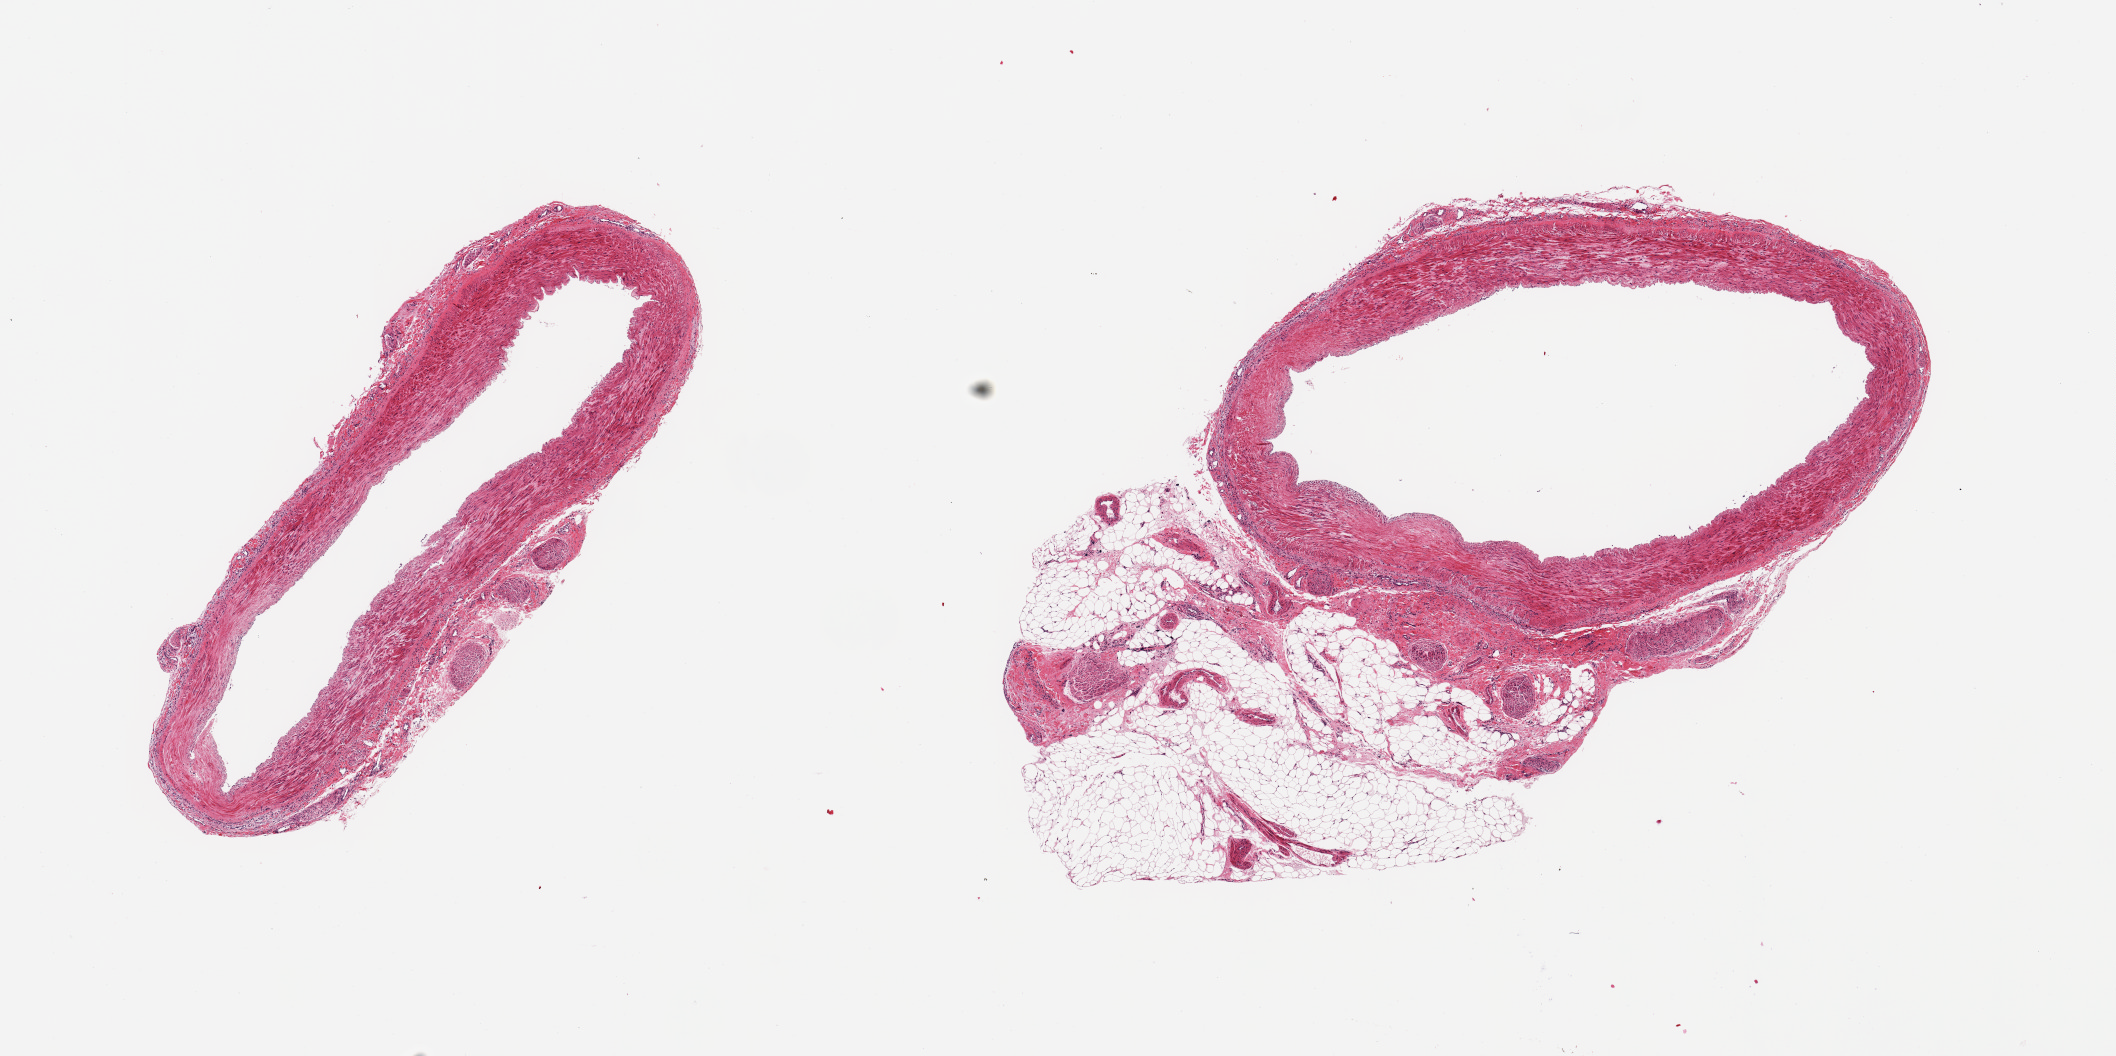
Whole-slide image, H&E stain — low-resolution overview of the scanned area, about 16.7 x 8.4 mm. PAXgene-fixed paraffin-embedded (PFPE) section. Target tissue: pancreas. Tissue donor sample. Donor sex: male.
* review note (as recorded): 2 pieces, sections of artery, unknown provenance, no pancreas